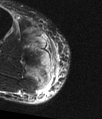
MRI of an extremity soft-tissue mass, one axial slice. T2-weighted fat-saturated. MR volume resampled by the dataset authors to the PET/CT grid (not the native acquisition matrix). 3.27 mm slice thickness. 102 × 119 image matrix, field of view 100 × 116 mm. Male patient. Case-level facts recorded for this patient, not image findings: histological type: pleiomorphic liposarcoma; grade: high; site of the primary tumour: right calf.
Structures marked on this image (expert contour drawn on MRI and transferred to this co-registered scan by the dataset authors):
- gross tumour volume including surrounding oedema: bounding box (x1, y1, x2, y2) in pixels: (49, 46, 54, 56)